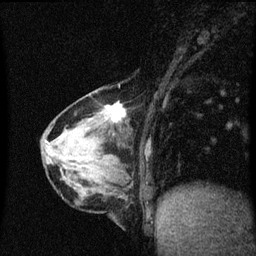
Breast MRI (dynamic contrast-enhanced), one sagittal slice; slice 17 of 60 in the series (ordered by position); dynamic contrast-enhanced series, image 2 of 3 at this slice position (ordered by acquisition); 1.5 T; TE 4.2 ms, TR 8.4 ms; 256 × 256 image matrix, field of view 200 × 200 mm. Female patient, age 64 years. Case-level facts recorded for this patient, not image findings: setting: breast cancer imaged before/during neoadjuvant chemotherapy; receptor status: HR-positive, HER2-negative.
Outlined on this slice (semi-automatically segmented with operator editing):
- analysis volume of interest (the breast-tissue region the enhancement analysis was run in; not a lesion): bounding box <65,96,127,157> (left, top, right, bottom; pixels)
- tumour enhancement mask (voxels above the 70 % enhancement threshold inside the analysis volume of interest): <107,104,126,121>